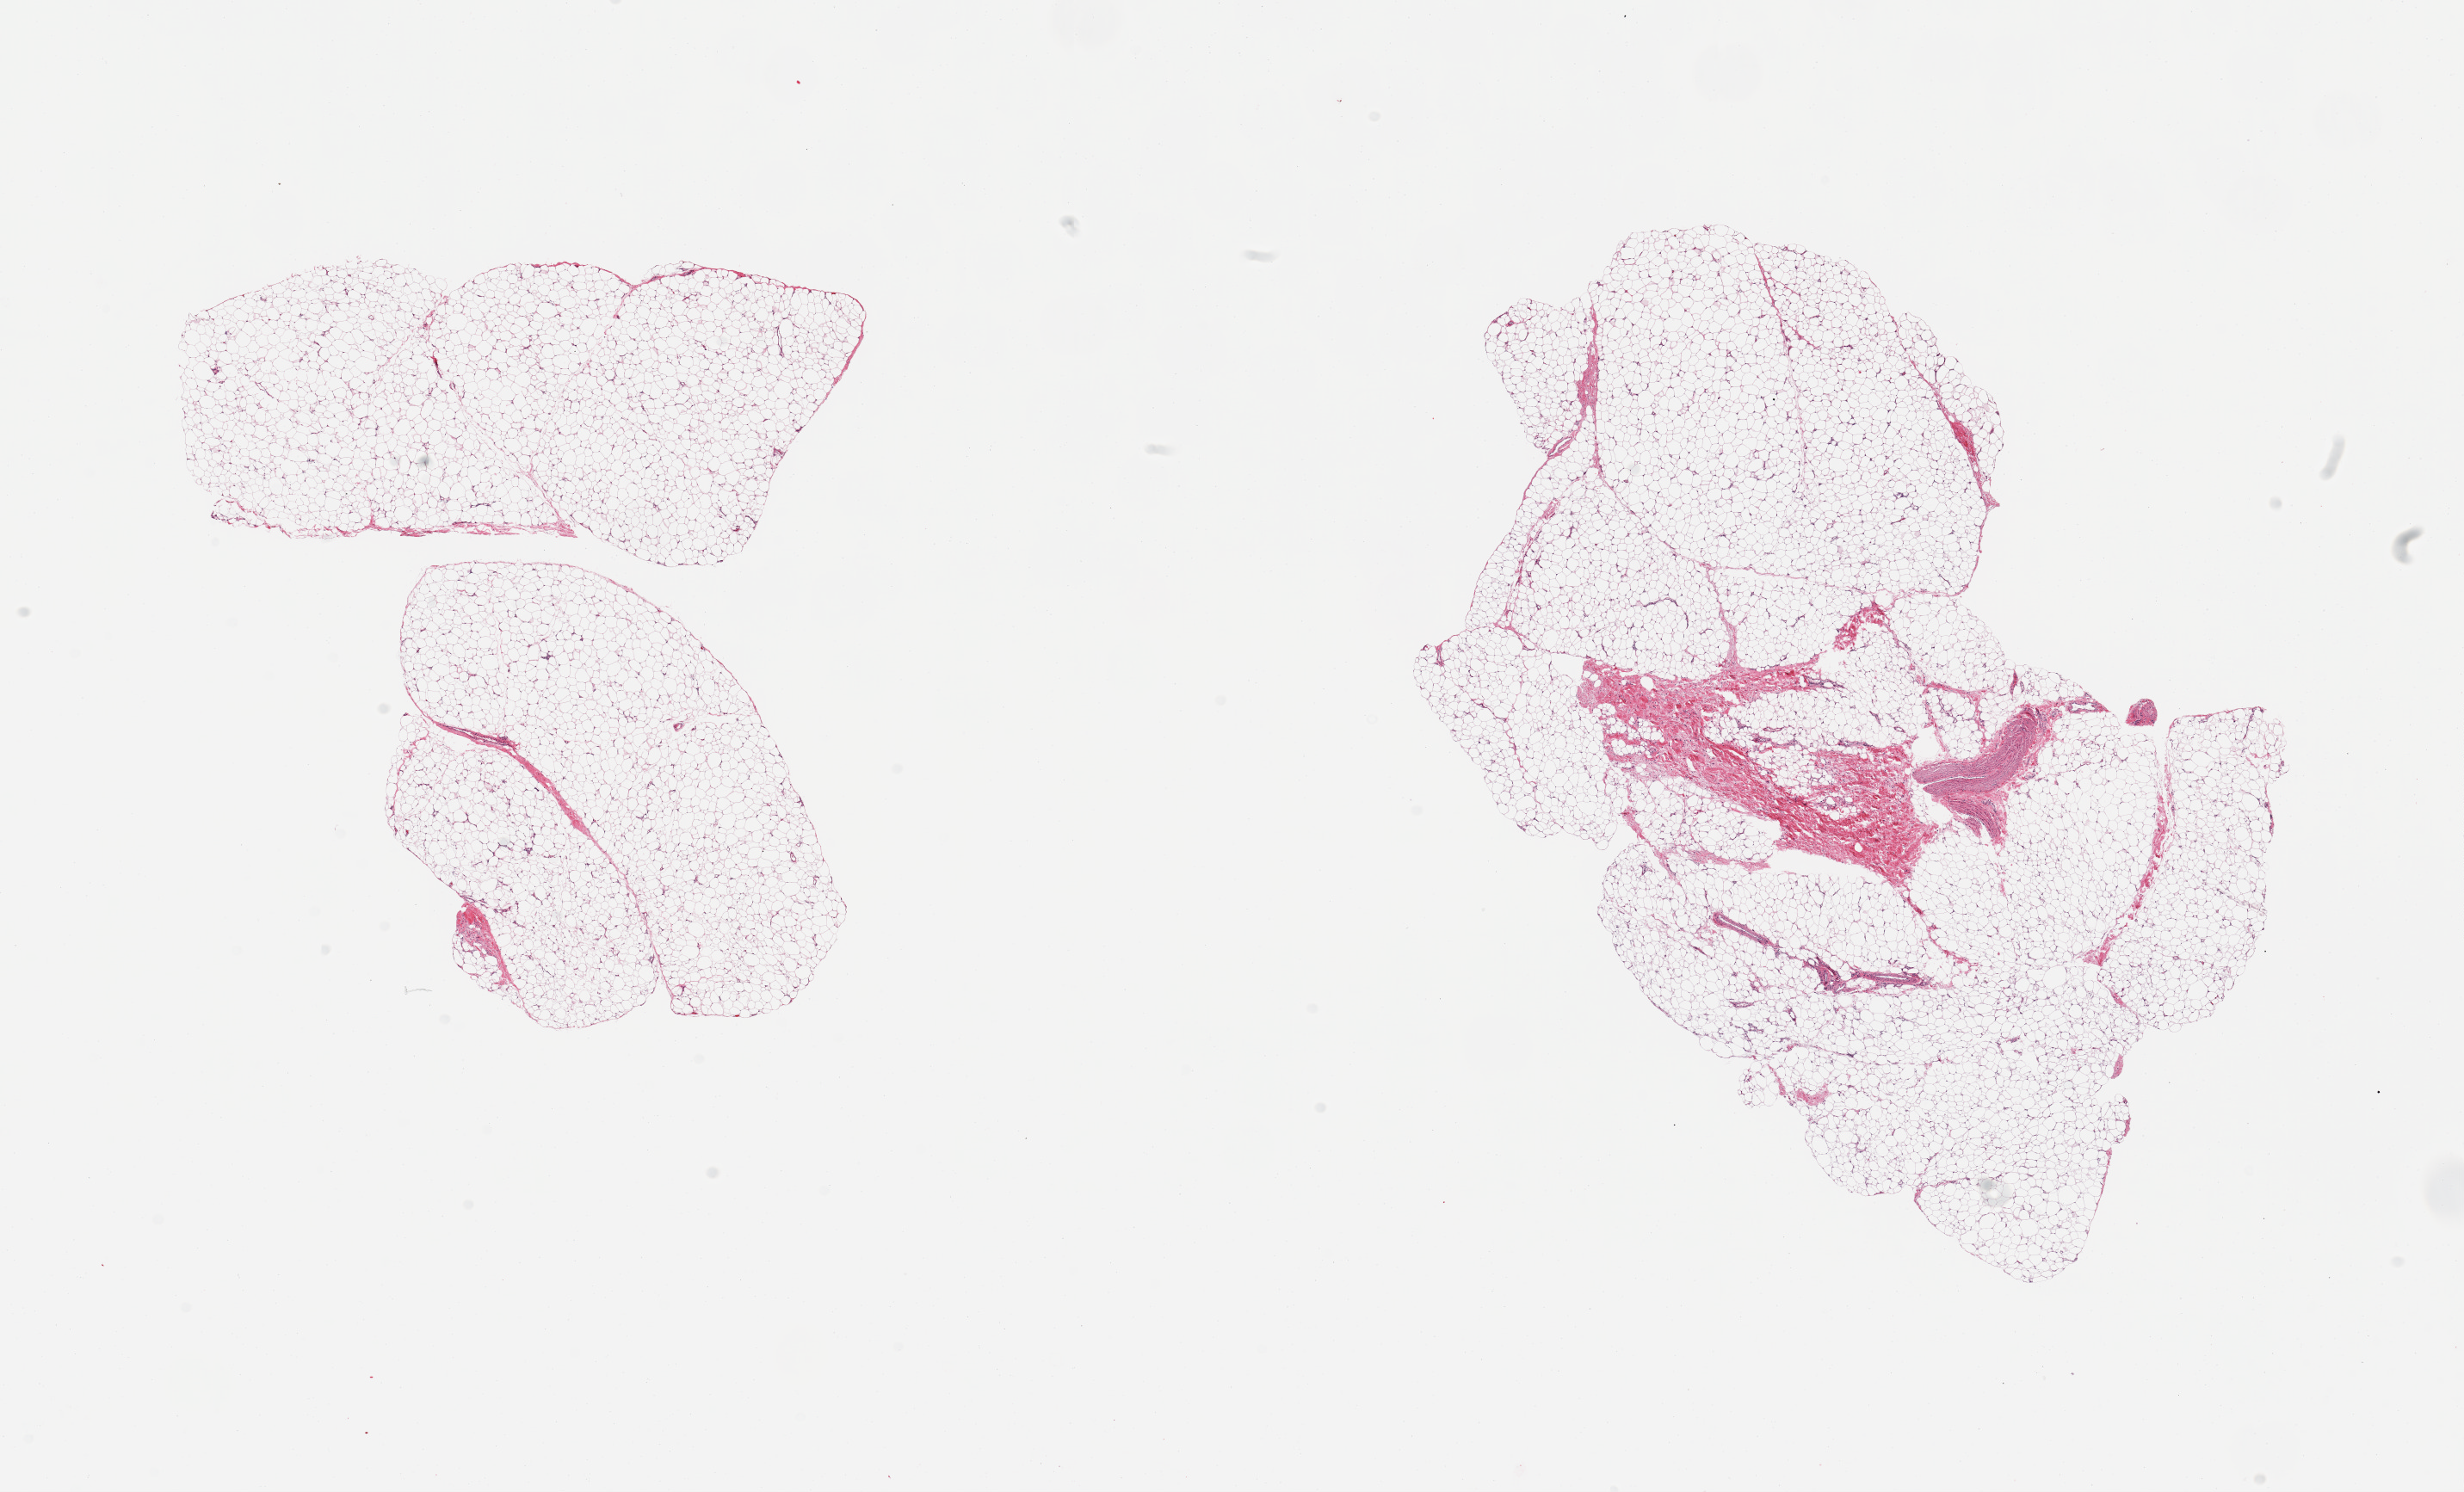
Digitized H&E-stained section, brightfield — shown as a low-resolution overview of the whole scanned area (about 22.6 x 13.7 mm); PAXgene-fixed paraffin-embedded (PFPE) section; section of adipose tissue (target tissue); donor tissue sample. Female donor.
Review note (as recorded): 2 pieces; one includes small amount of fibrous tissue and portion of large vessel.